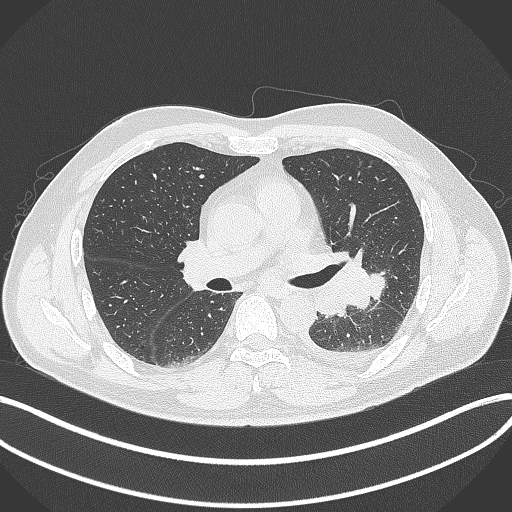
Chest CT, one axial slice; position 203 of 342 along the scan axis; 120 kVp; lung window (W 1500 / L -600 HU); 1 mm slice thickness; 512 × 512 image matrix. Patient: male, 58 years. From the clinical record (not read from this slice): clinical TNM (as recorded): T3 N1 M1b.
Annotated regions visible in this slice (bounding box drawn by a radiologist):
- lung tumour (recorded histology: small cell carcinoma): bounding box [x1, y1, x2, y2] px = [347, 257, 386, 308]